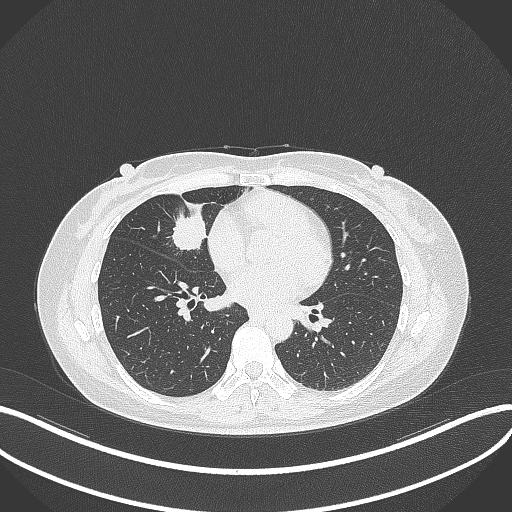
Chest CT, one axial slice. Slice 129 of 284 in the series (ordered by position). Reconstruction kernel B70f. Lung window (W 1500 / L -600 HU). 1 mm slice thickness. 512 × 512 image matrix. Female patient, age 43 years. From the clinical record (not read from this slice): clinical TNM (as recorded): T1c N3 M1; histopathological grade: G1.
Annotated regions visible in this slice (bounding box drawn by a radiologist):
- lung tumour (recorded histology: adenocarcinoma): bounding box [x1, y1, x2, y2] px = [169, 205, 208, 255]